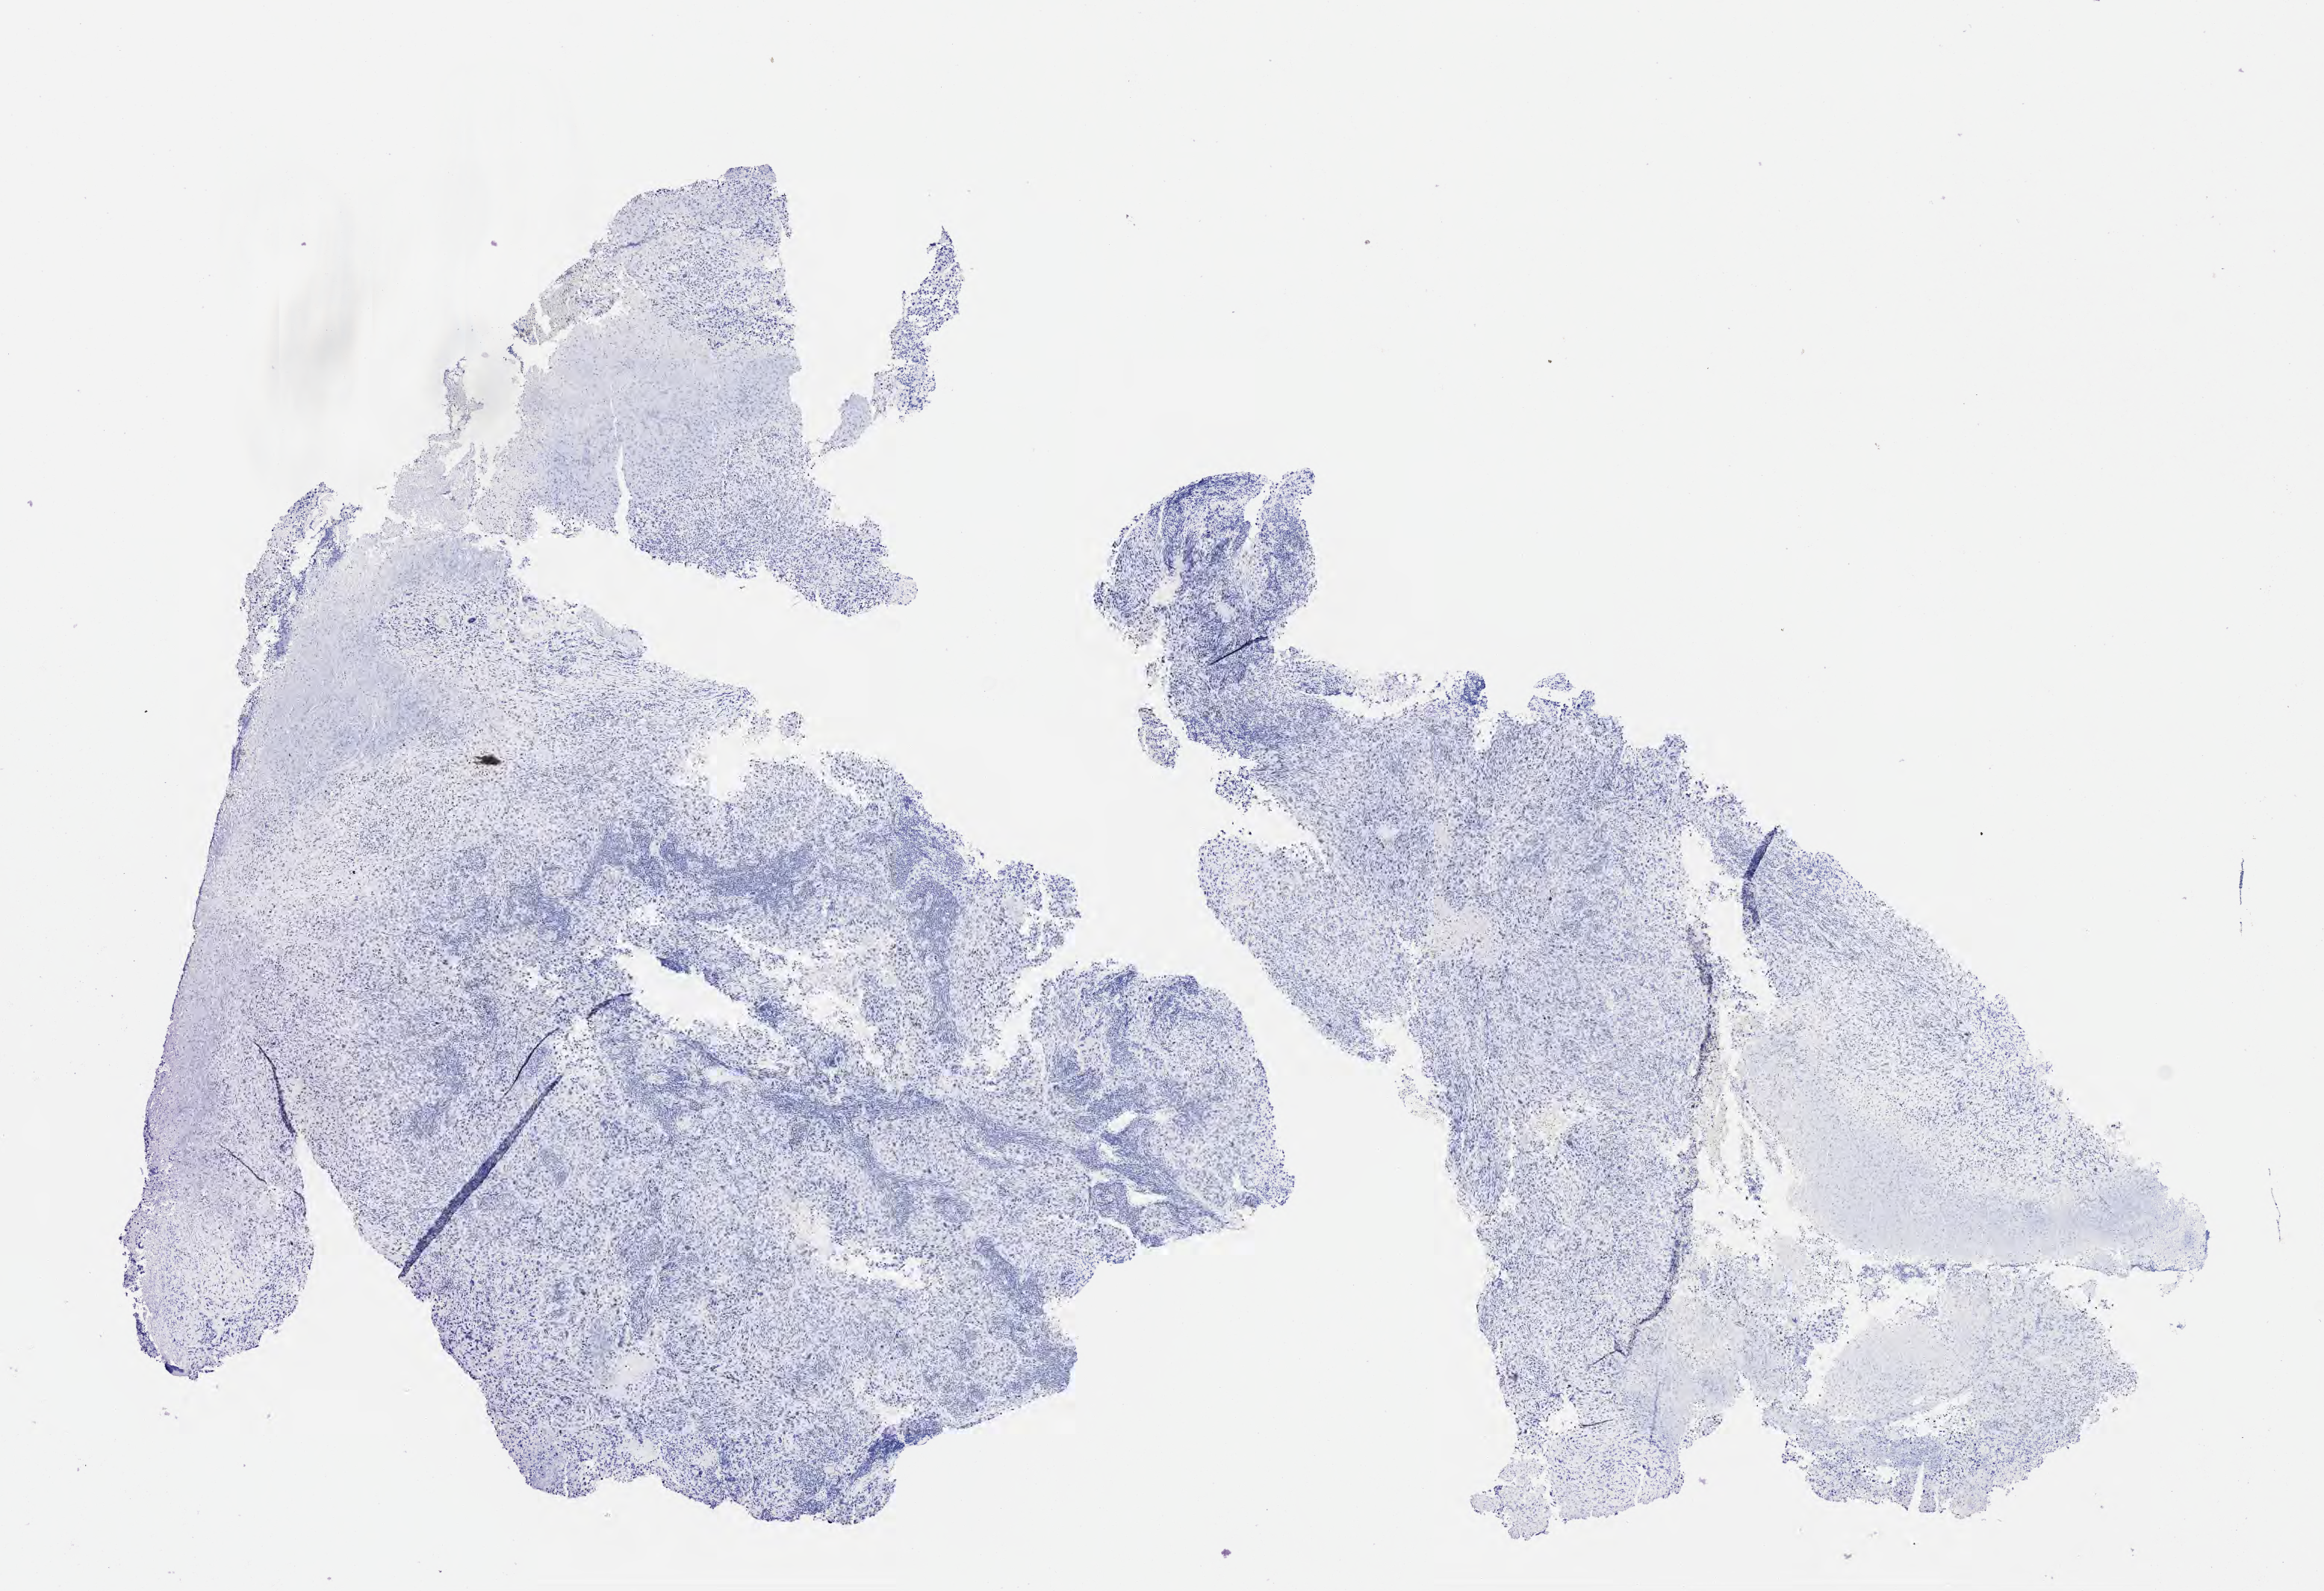
Immunohistochemistry (IHC) whole-slide image stained for MOC-31 (anti-EpCAM) — shown as a low-resolution overview of the whole scanned area (about 12.6 x 8.6 mm); specimen: tumor tissue; site: cervix. Patient female; 38 years old.
- diagnosis: Squamous cell carcinoma, large cell, nonkeratinizing, NOS